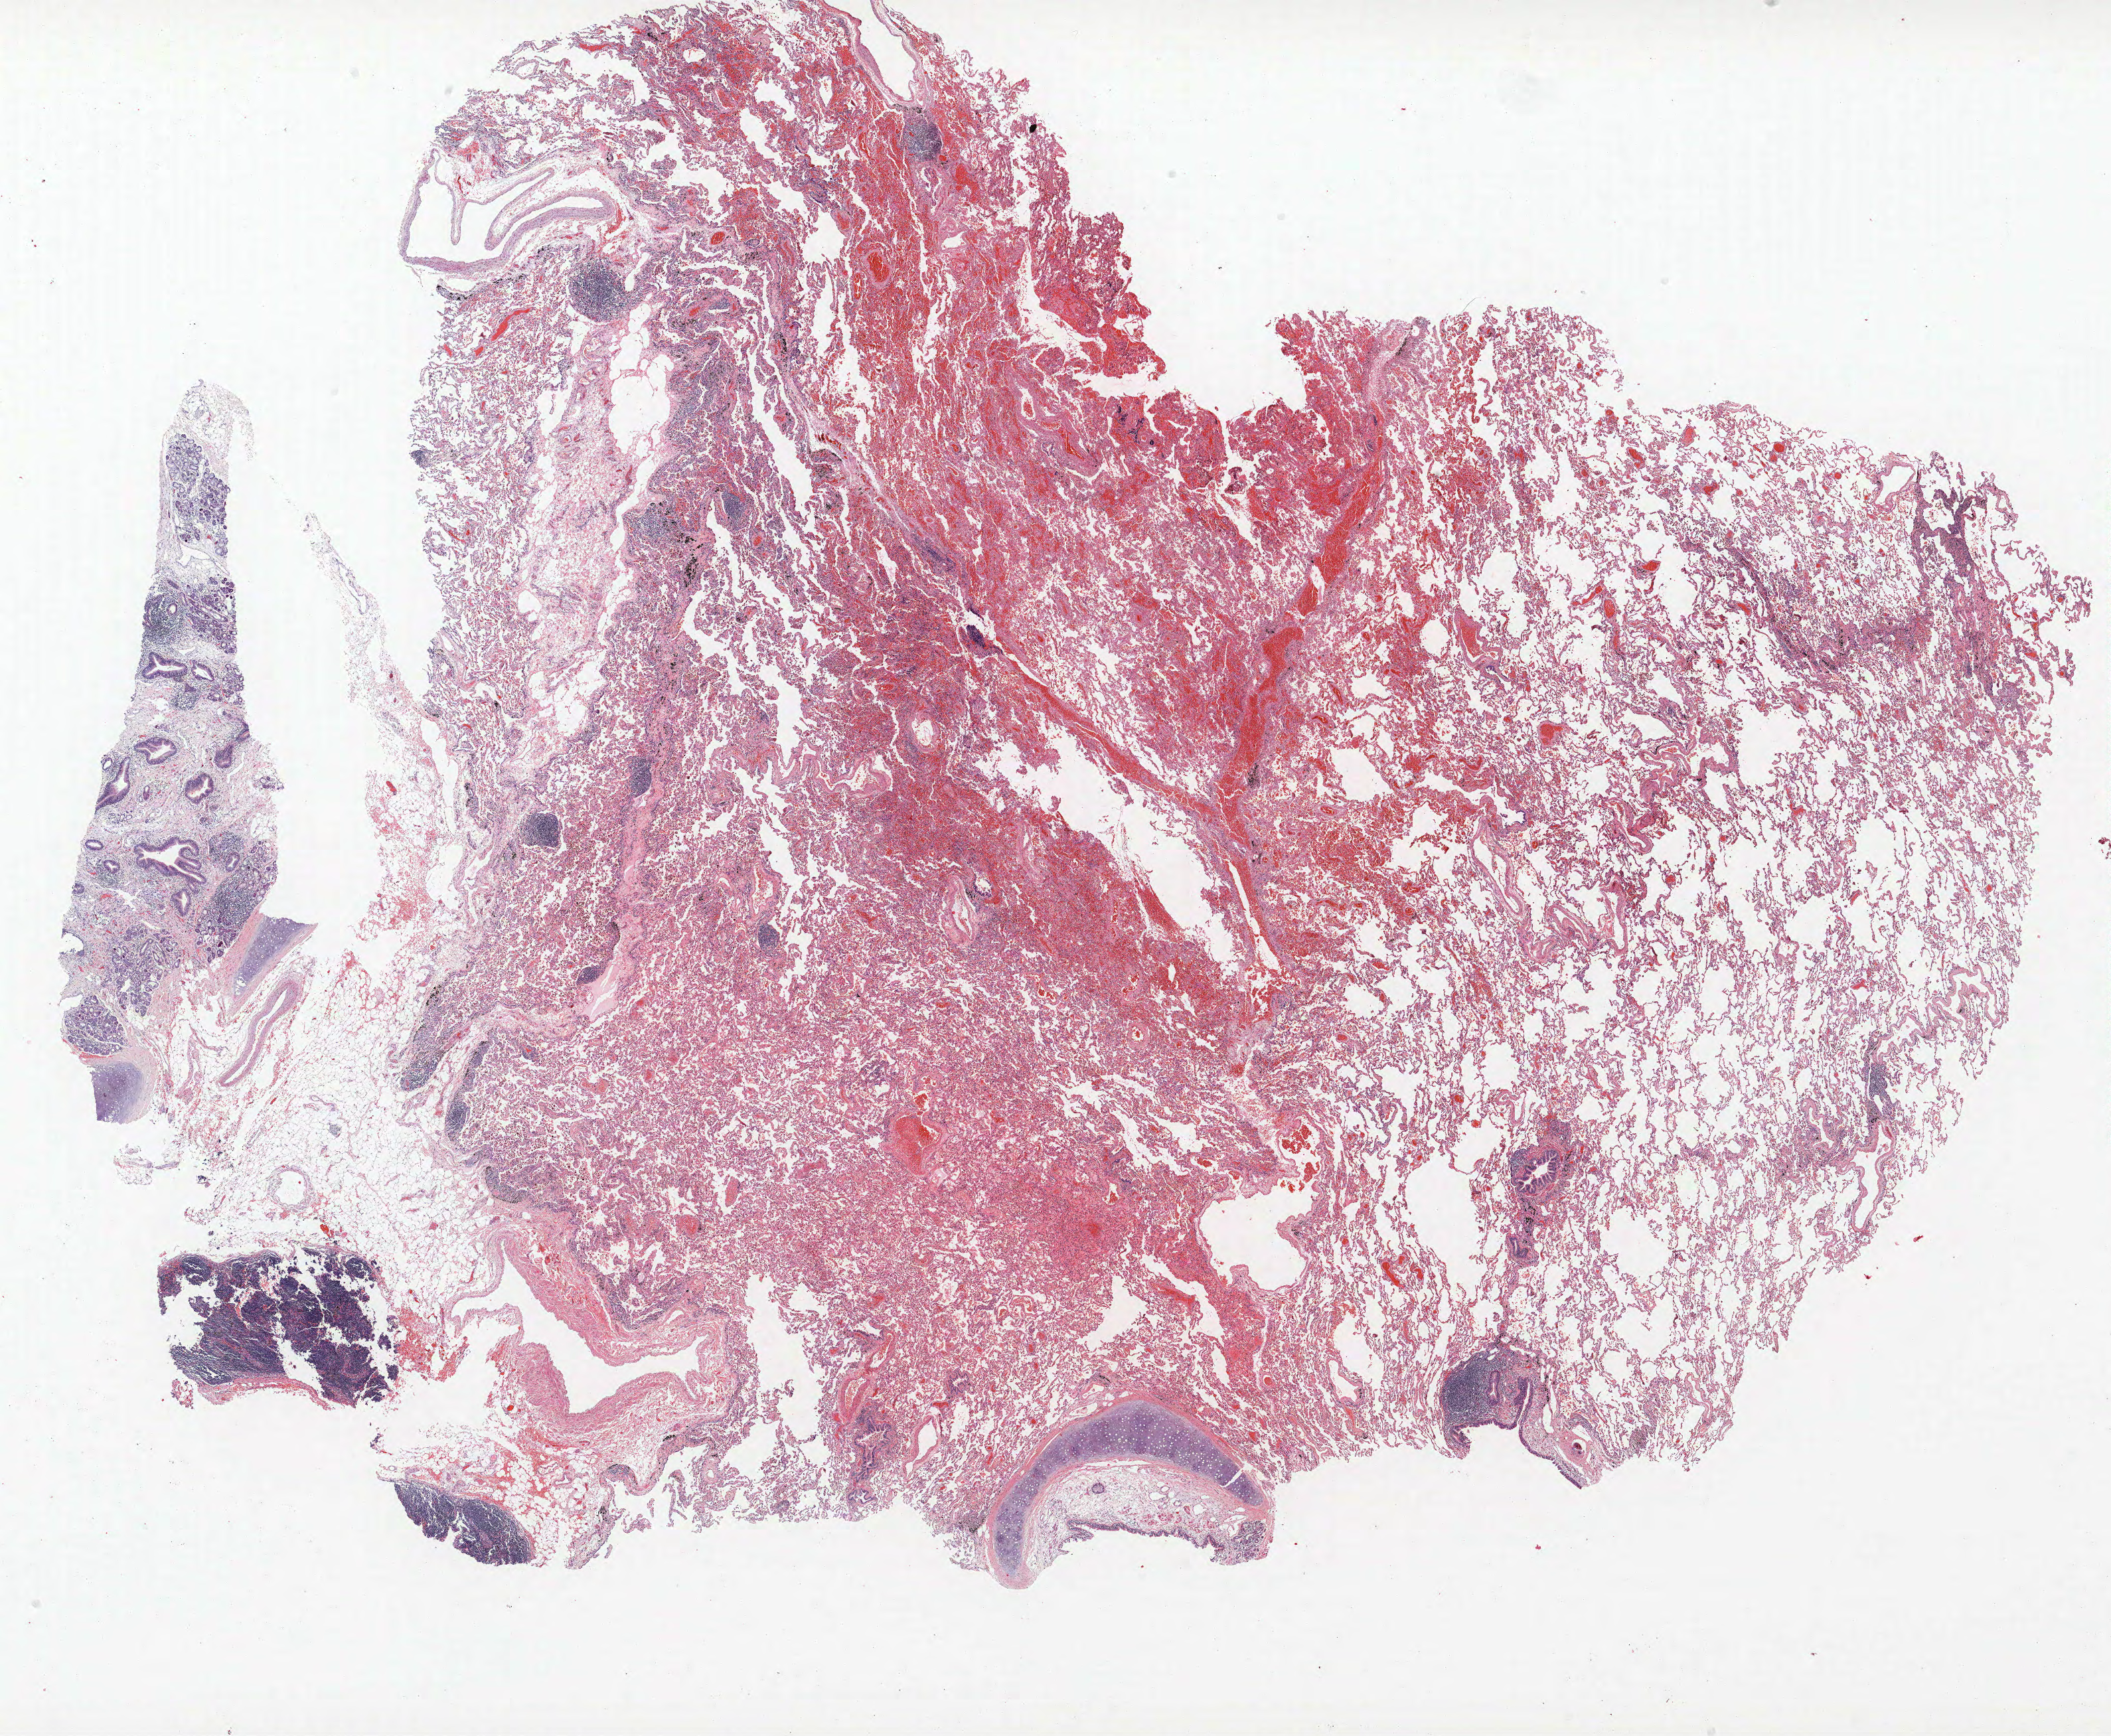
Whole-slide histology image, Hematoxylin and eosin (H&E) stained — shown as a low-resolution overview of the whole scanned area (about 25.4 x 20.9 mm, acquisition: 40x scan), formalin-fixed paraffin-embedded (FFPE) section, lung. Male, age 65 at enrolment. Grade: moderately differentiated (G2).
Primary tumour location (clinical record): left upper lobe. Participant's lung-cancer diagnosis: Adenocarcinoma, NOS (ICD-O-3 8140/3). Stage (AJCC 6th edition): IA. Tumour size (pathology): 10 mm.